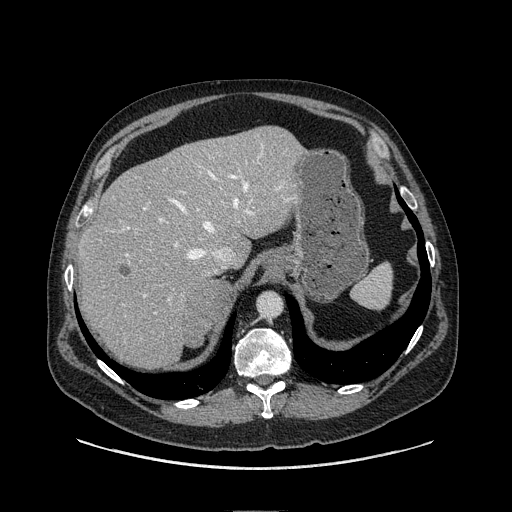
Contrast-enhanced abdominal CT, one axial slice; position 86 of 149 along the scan axis; soft-tissue window (W 400 / L 40 HU); 1.25 mm slice thickness; 512 × 512 image matrix, field of view 440 × 440 mm. Male patient. Case-level facts recorded for this patient, not image findings: diagnosis: adrenocortical carcinoma; tumour side: right adrenal; tumour size at pathology: 7.5 cm; Ki-67 index: 15 %; stage (as recorded): 2.
Structures marked on this image (semi-automatic segmentation, software-assisted and operator-edited):
- mass: bounding box (x1, y1, x2, y2) in pixels: (183, 282, 230, 344)